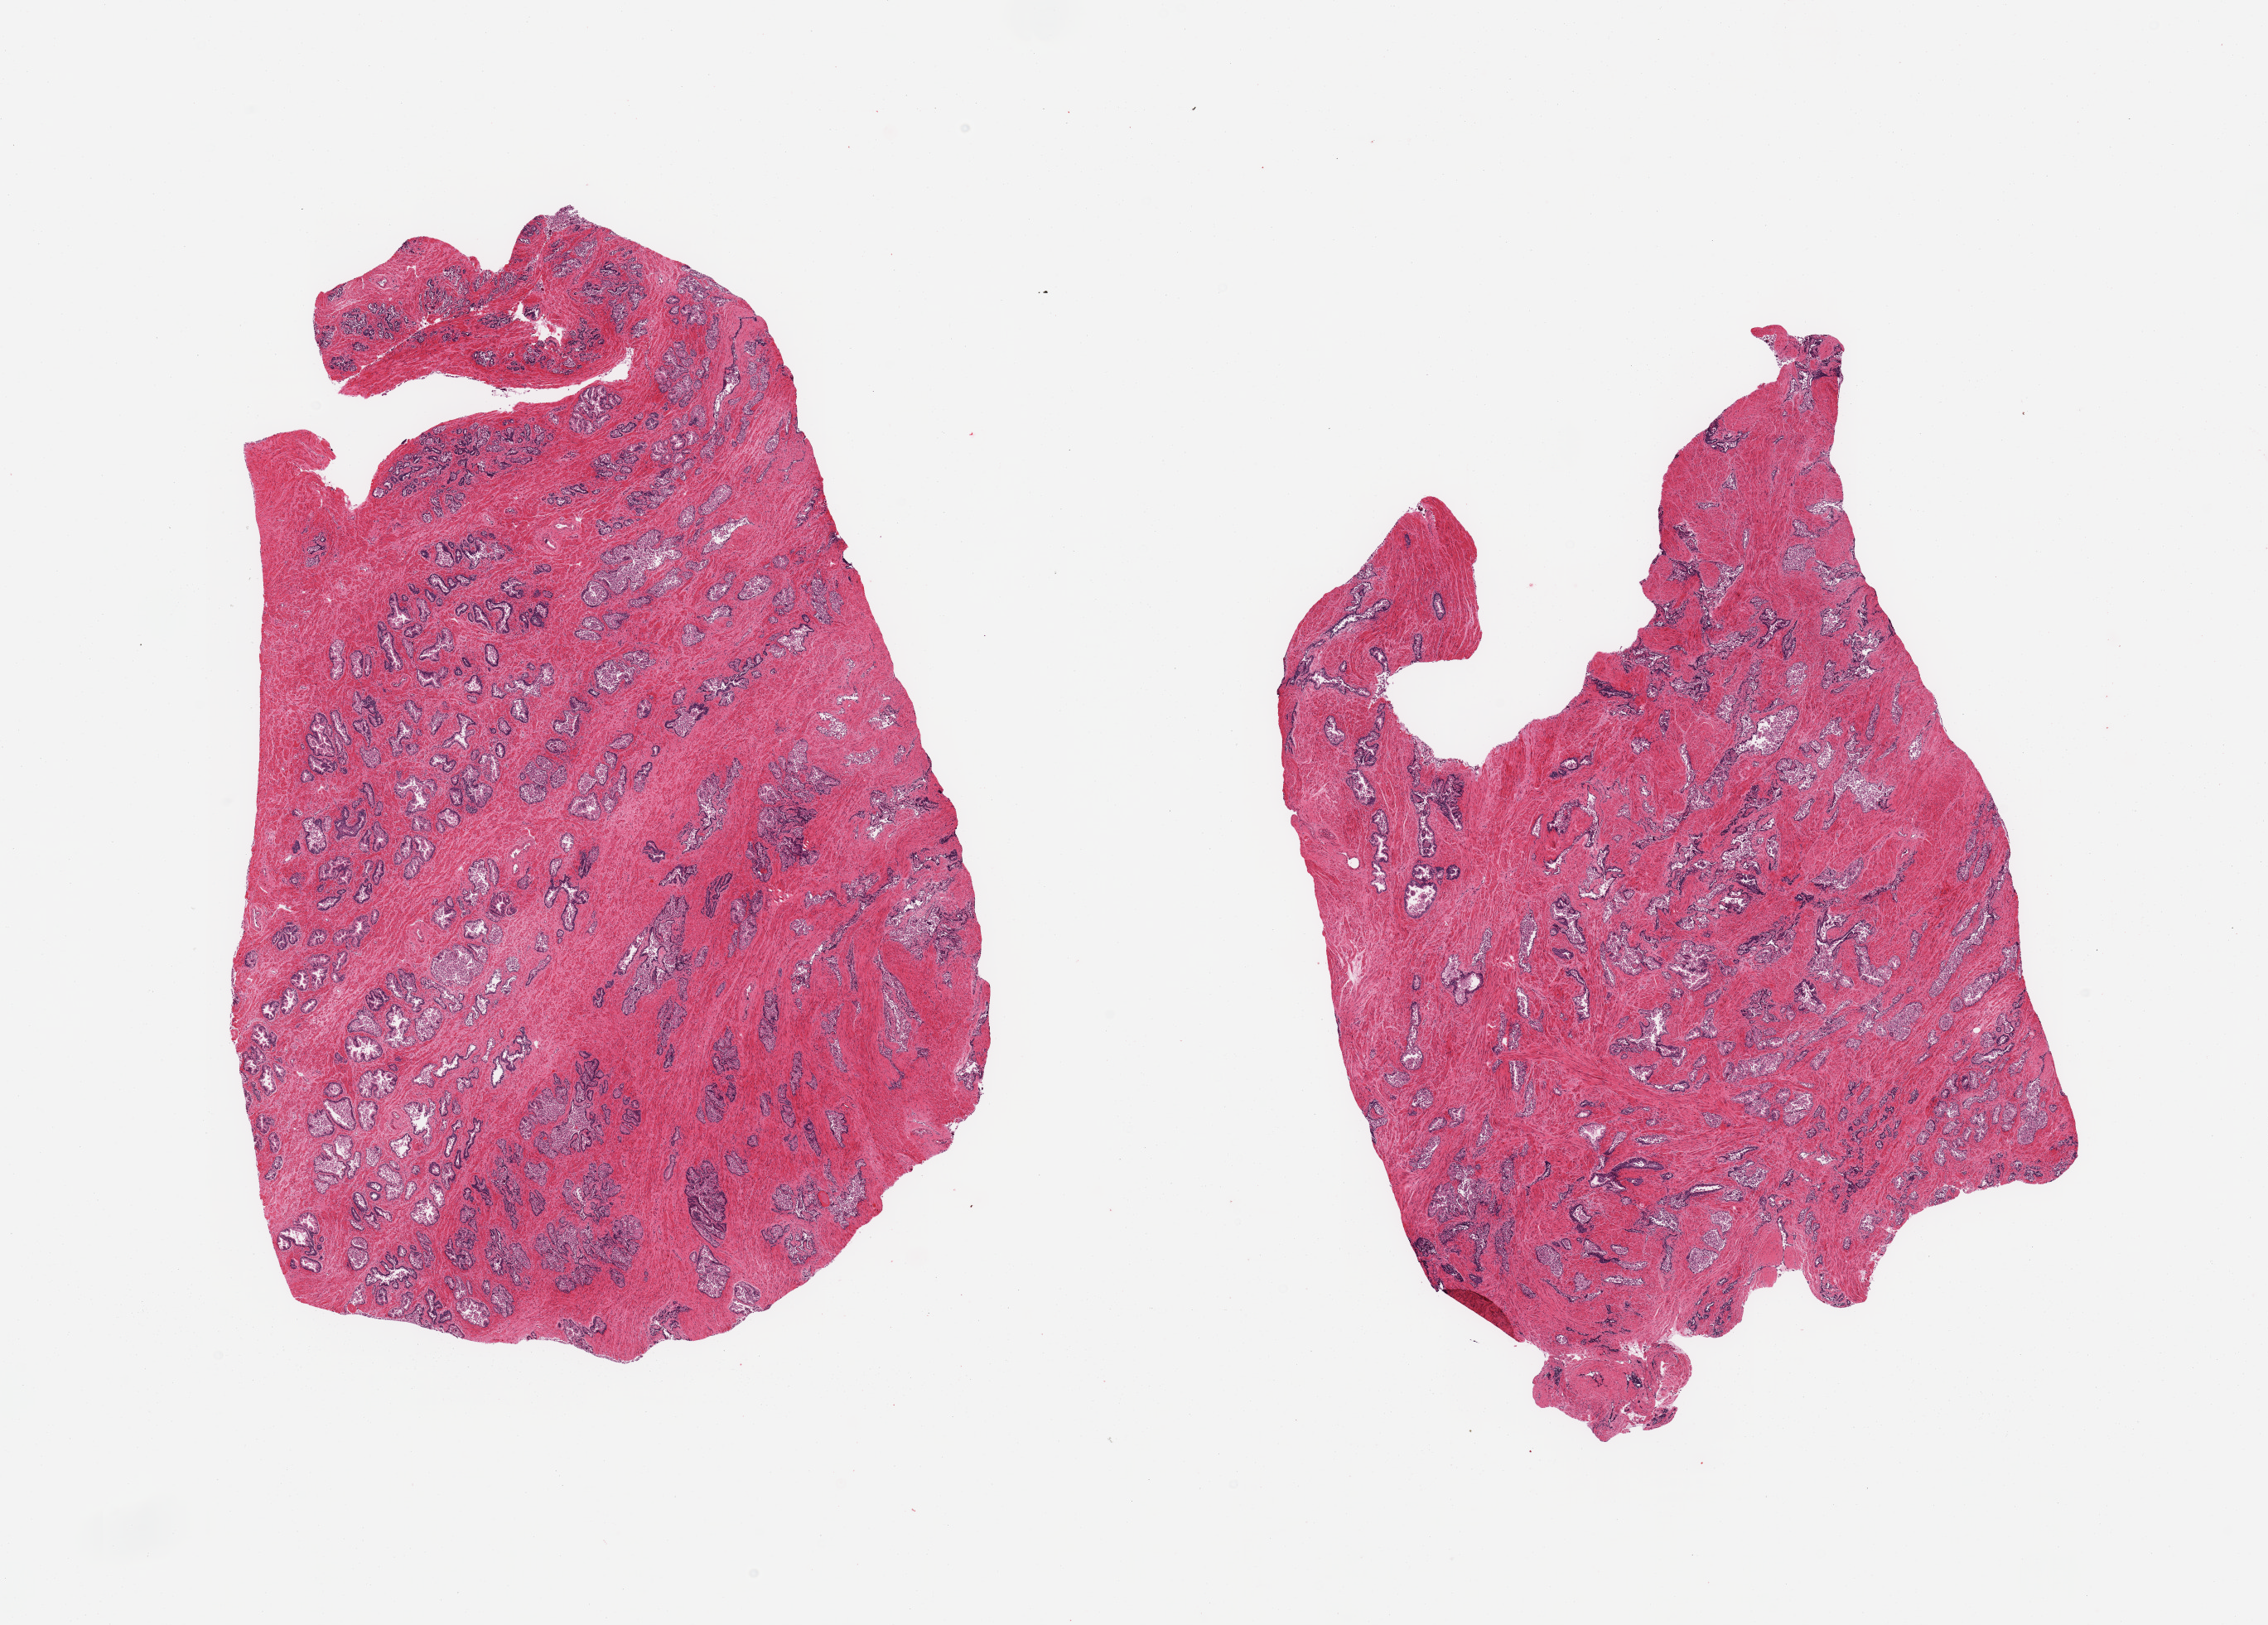
Digitized haematoxylin and eosin-stained section, brightfield, shown as a low-resolution overview of the whole scanned area (about 21.7 x 15.5 mm), PAXgene-fixed paraffin-embedded (PFPE) section, section of prostate (target tissue), donor tissue sample. Donor: male.
Pathologist's review note for this sample: 2 pieces; moderate desquamation of gland epithelium.